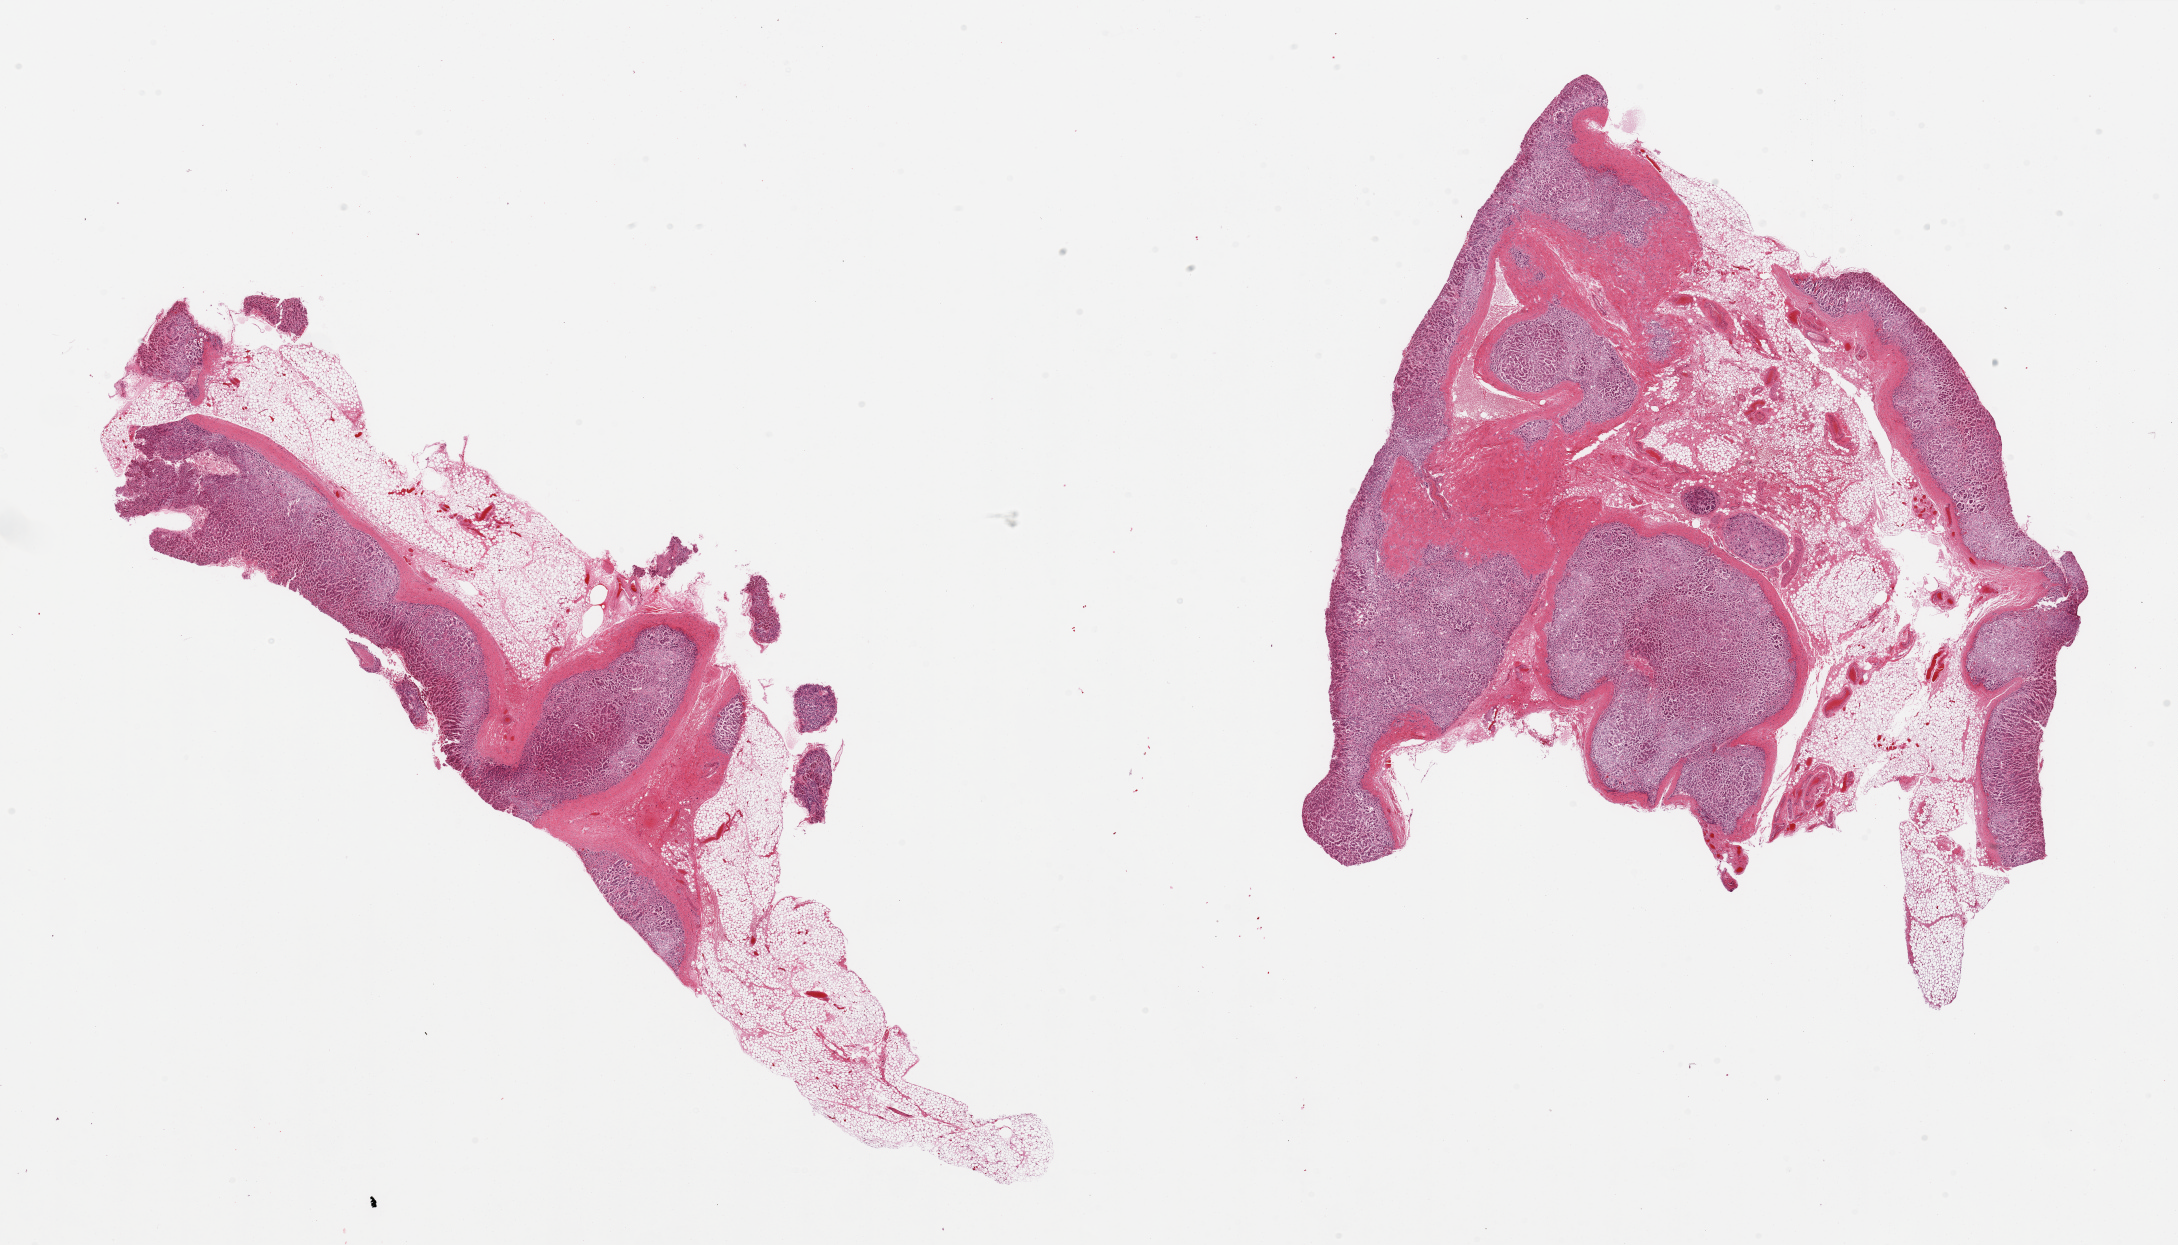
H&E whole-slide image, a low-resolution overview of the entire scanned area, about 34.5 x 19.7 mm (from a 20x scan), PAXgene-fixed paraffin-embedded (PFPE) section, sampled site (target tissue): adrenal gland, donor tissue sample. Donor sex: female.
Reviewer comment on this tissue sample: 2 pieces, ~50% adherent fat/stroma. All cortex, markedly autolyzed.